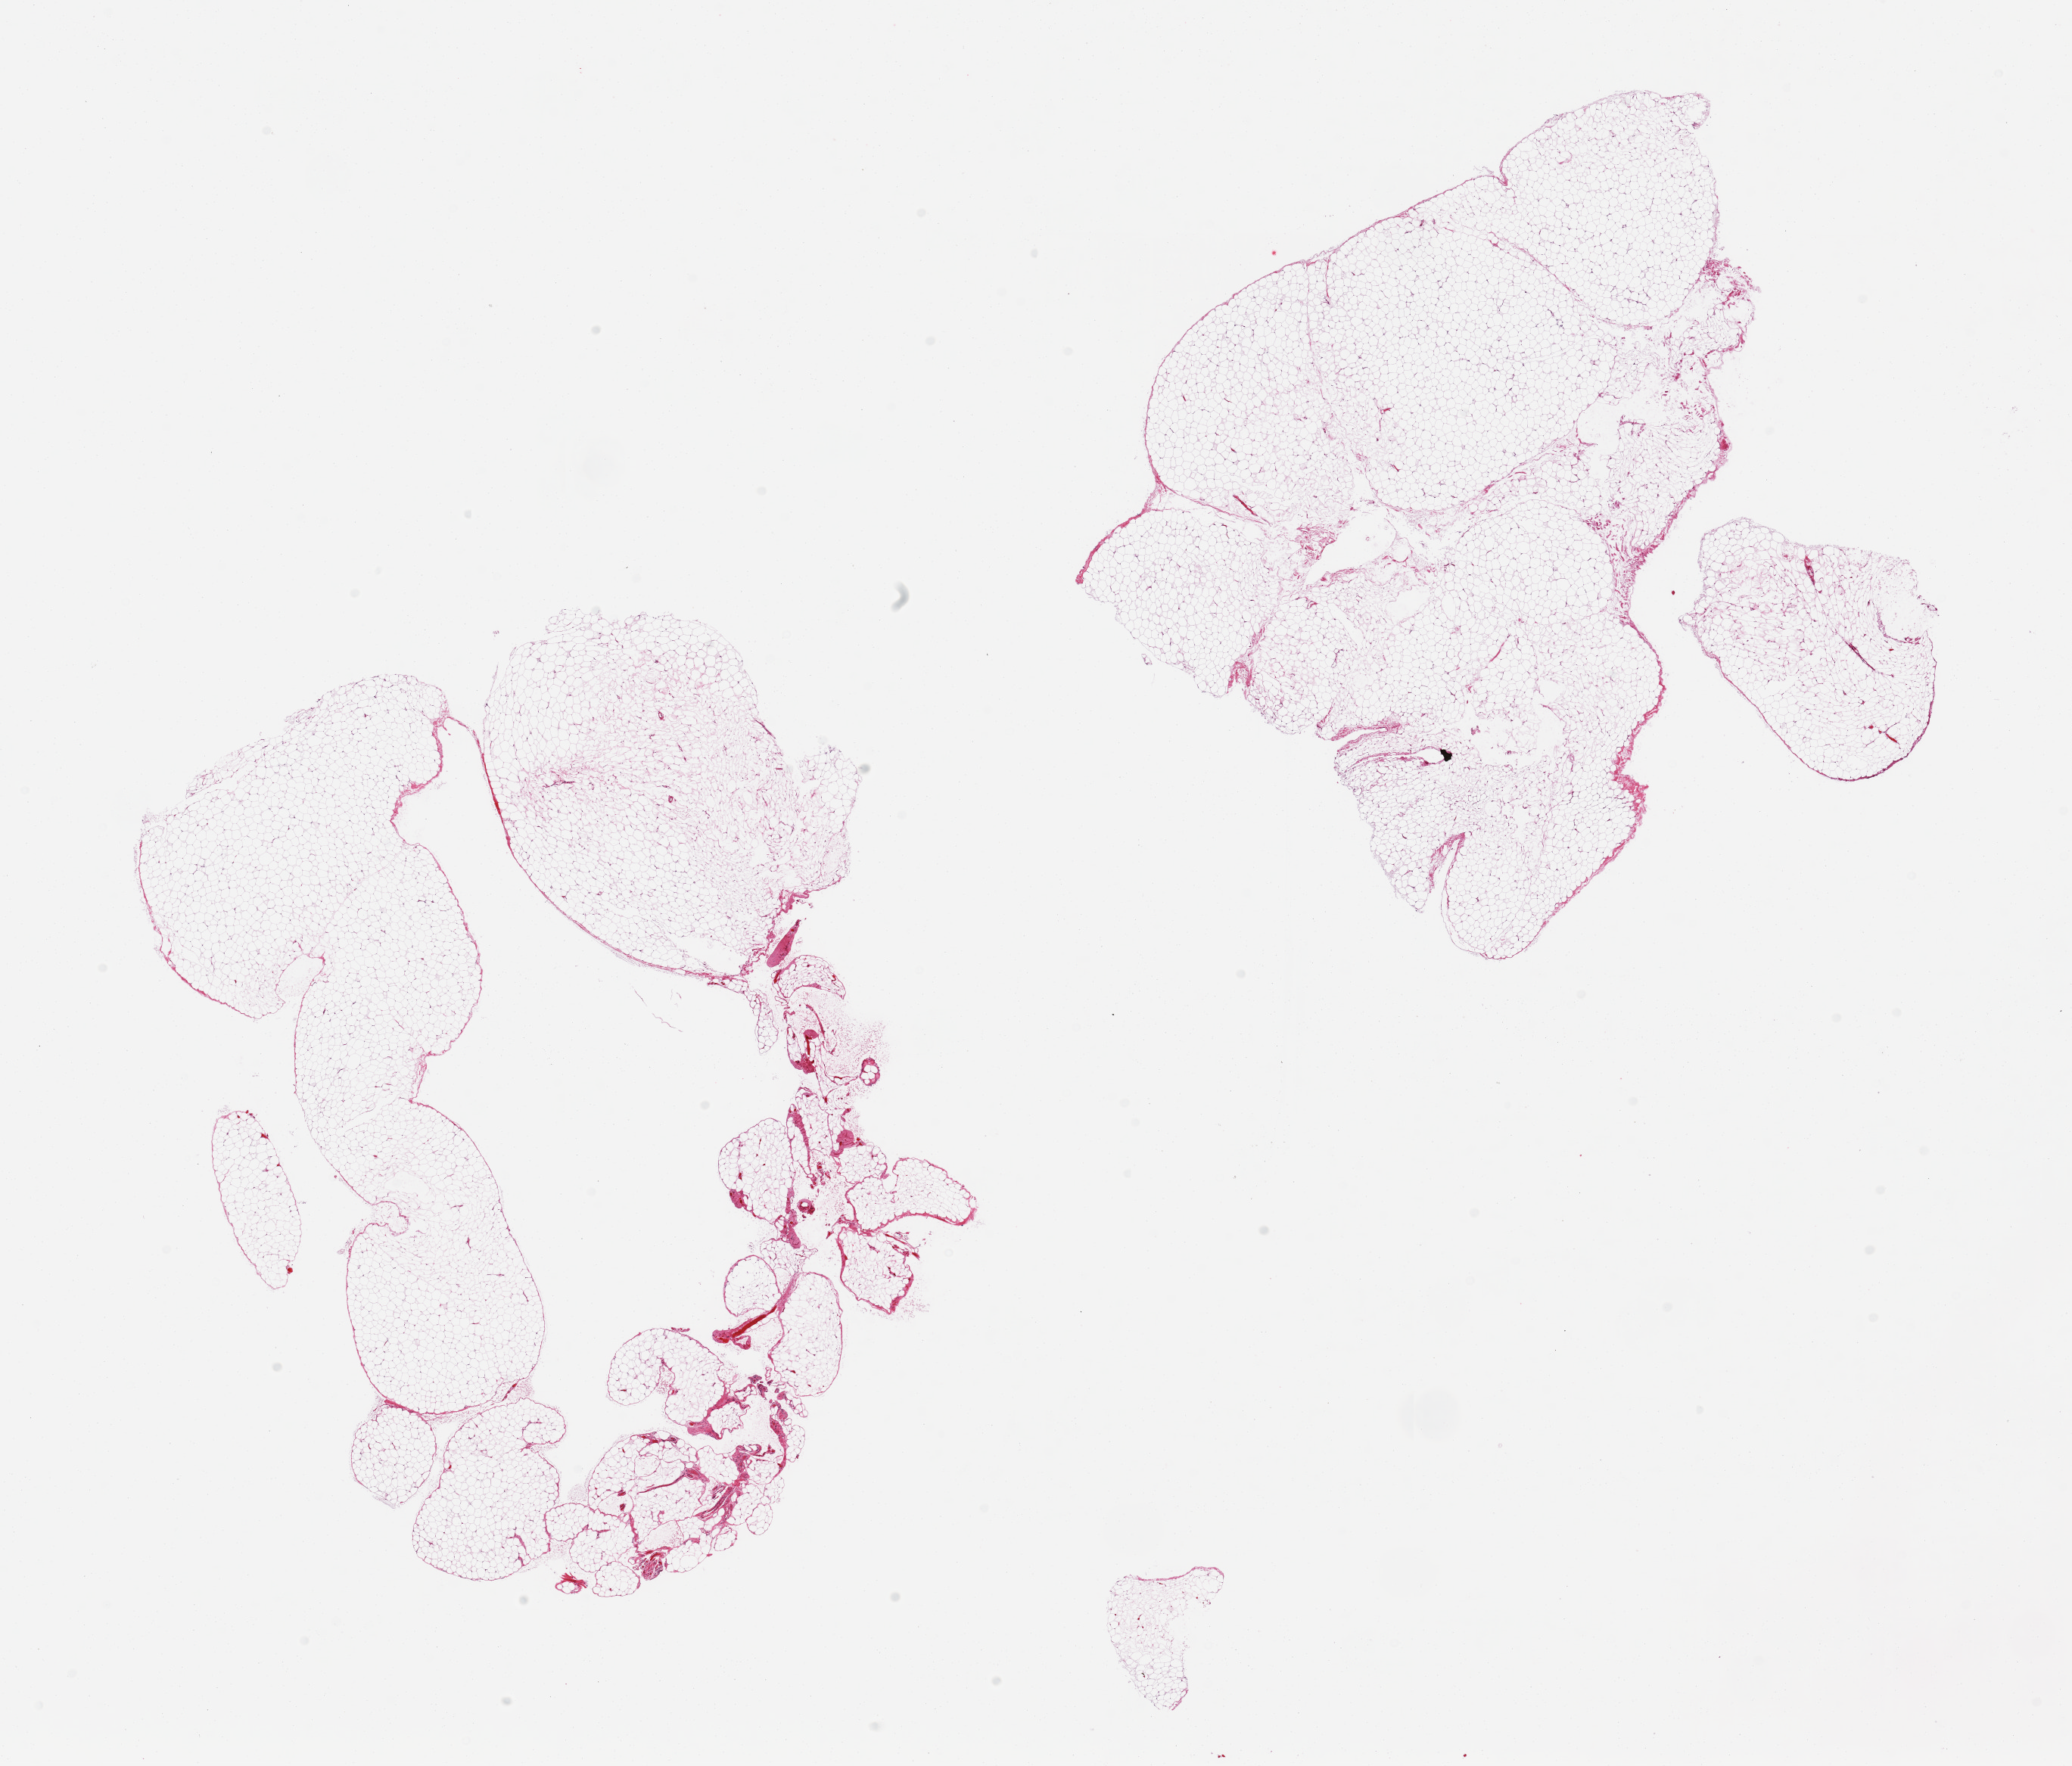
Digitized haematoxylin and eosin-stained section — whole scanned area (about 21.7 x 18.5 mm, acquisition: 20x scan) shown as a low-resolution overview. PAXgene-fixed paraffin-embedded (PFPE) section. Sampled site (target tissue): omentum. Tissue donor sample.
Reviewer comment on this tissue sample: 2 pieces, trace fascia.